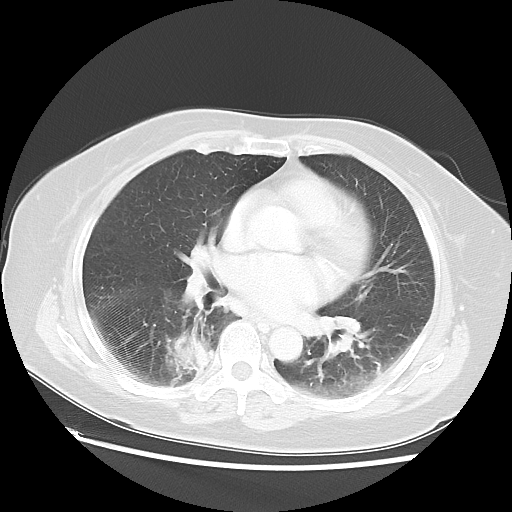
Chest CT, one axial slice. Lung window (W 1500 / L -600 HU). 512 × 512 image matrix, field of view 356 × 356 mm. Female patient, age 69 years. From the clinical record (not read from this slice): clinical TNM (as recorded): T2 N1 M1a.
Outlined on this slice (bounding box drawn by a radiologist):
- lung tumour (recorded histology: adenocarcinoma): box from (x=160, y=327) to (x=222, y=378) px